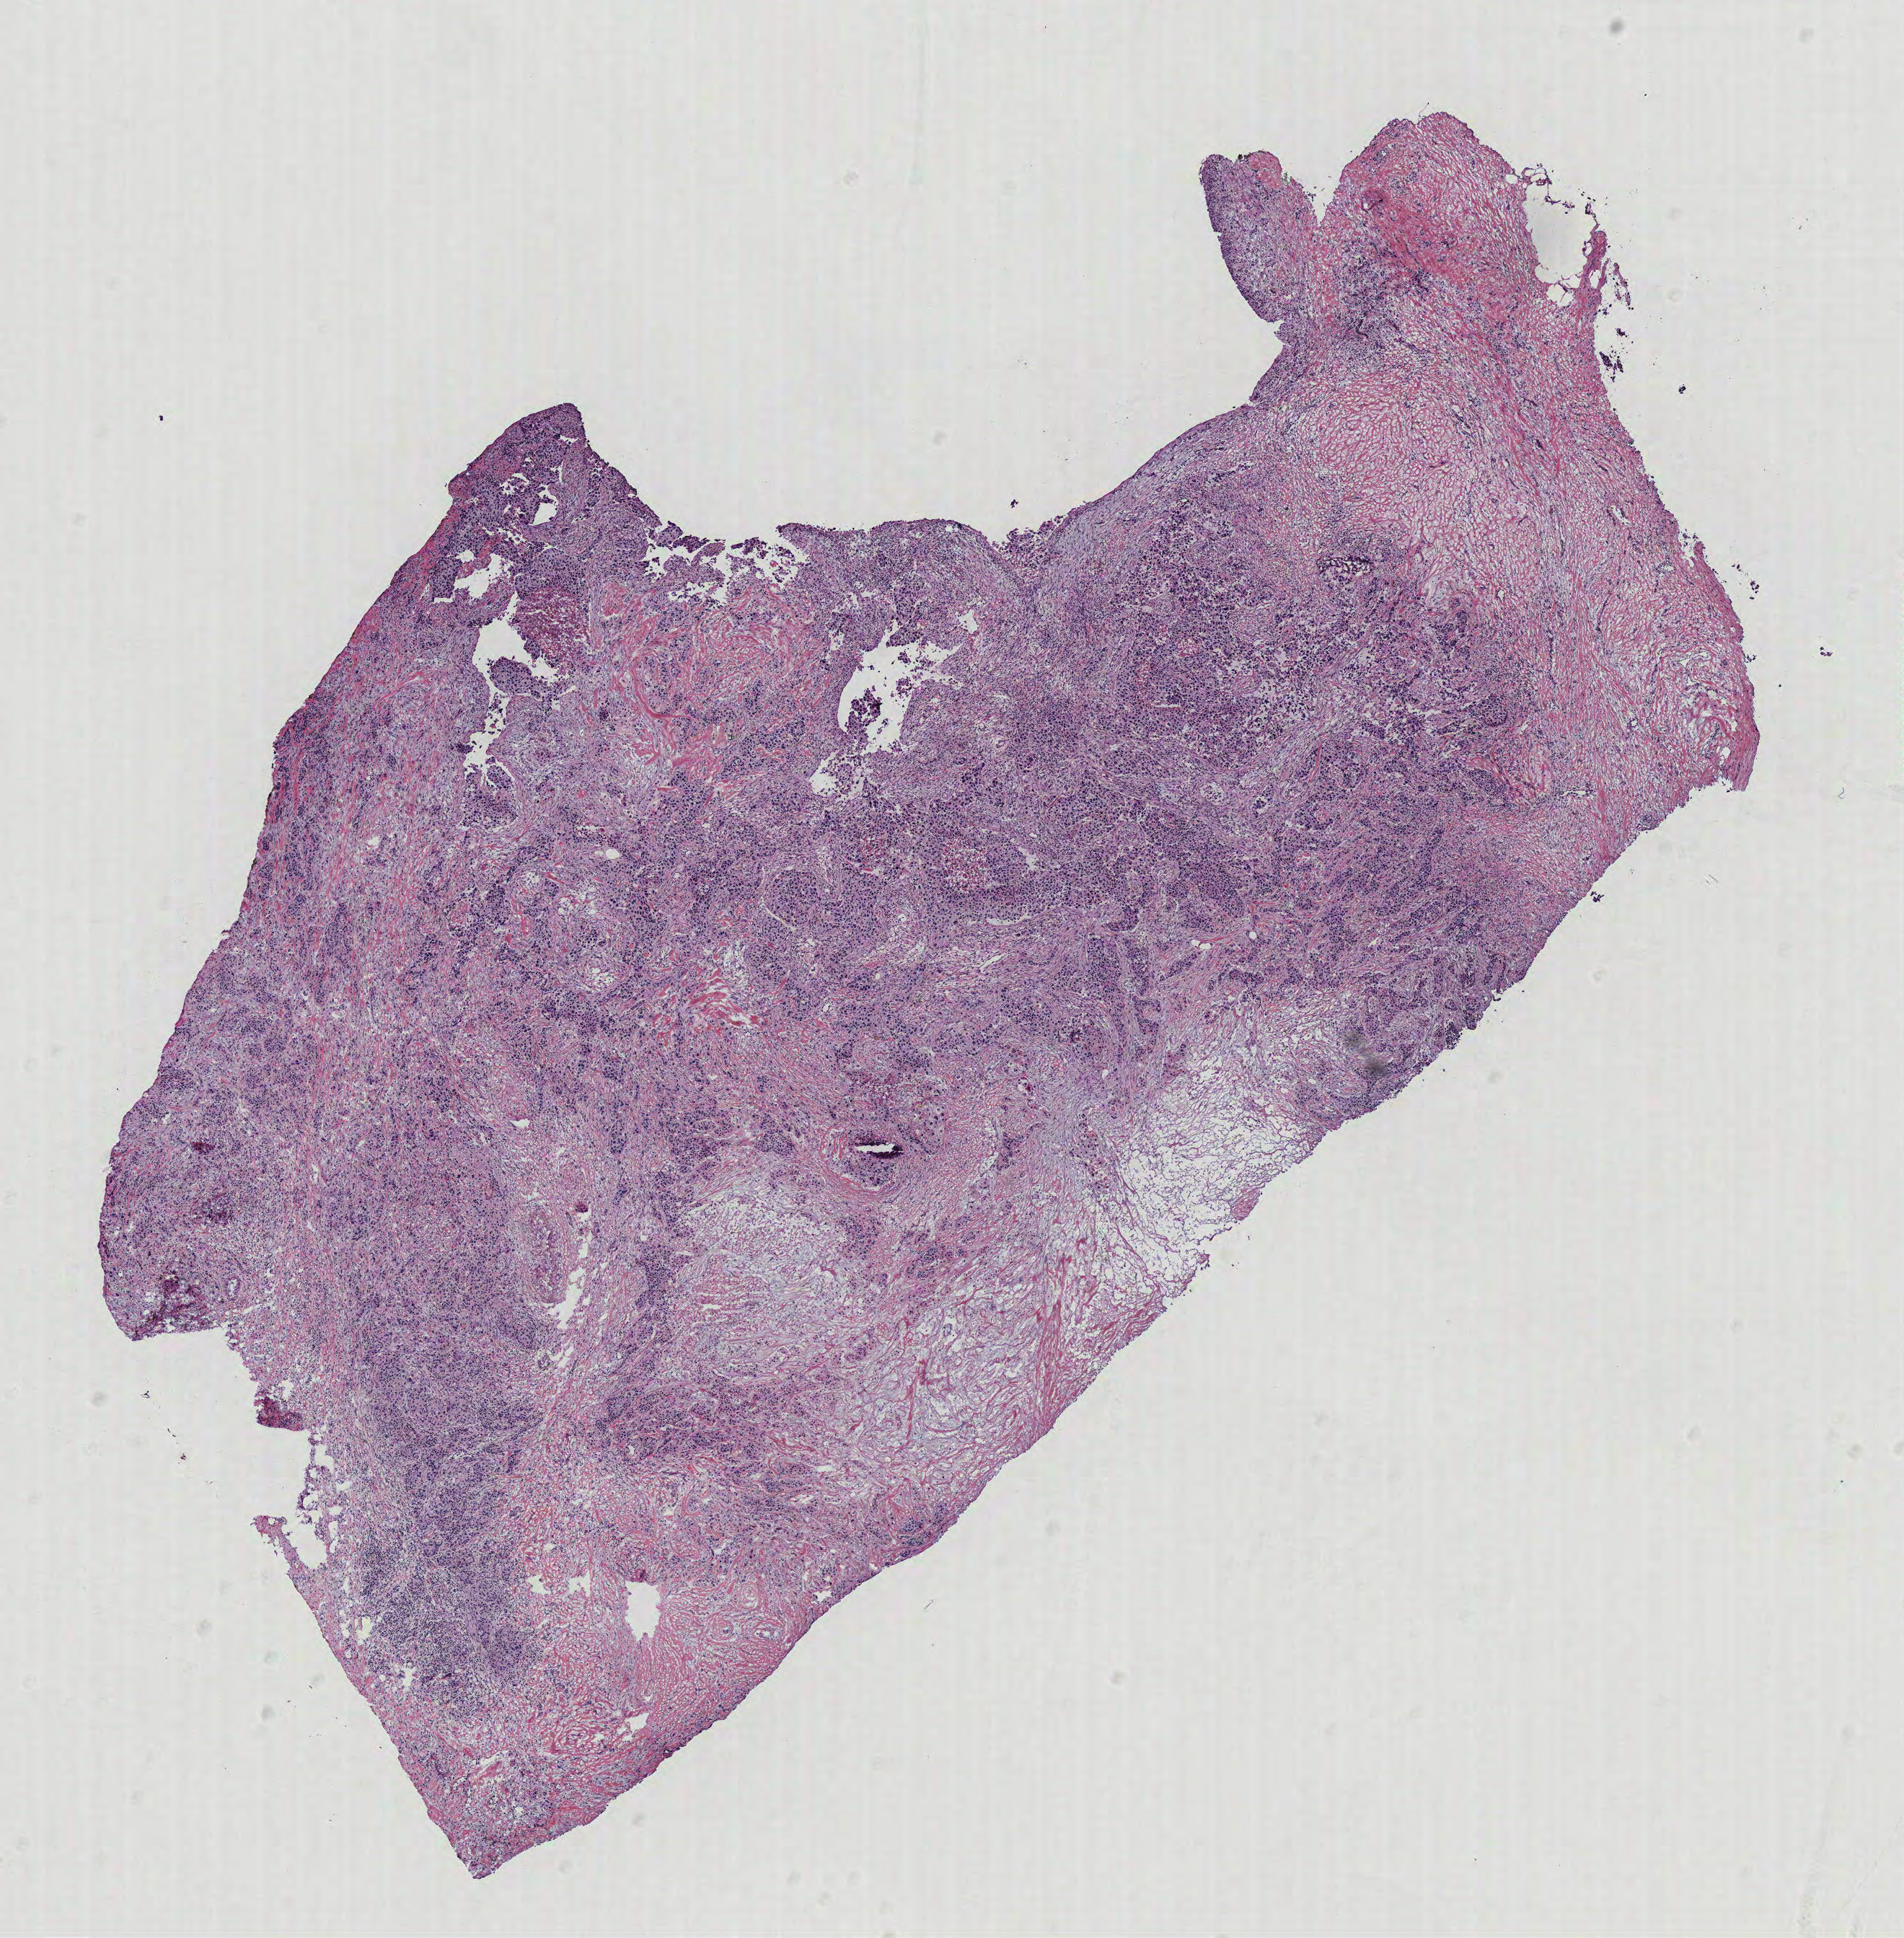
Whole-slide histology image, H&E-stained, whole scanned area (about 10.6 x 10.8 mm, from a 40x scan) shown as a low-resolution overview. Breast, tissue type not recorded.
• patient diagnosis (cohort enrolment): breast cancer (breast)